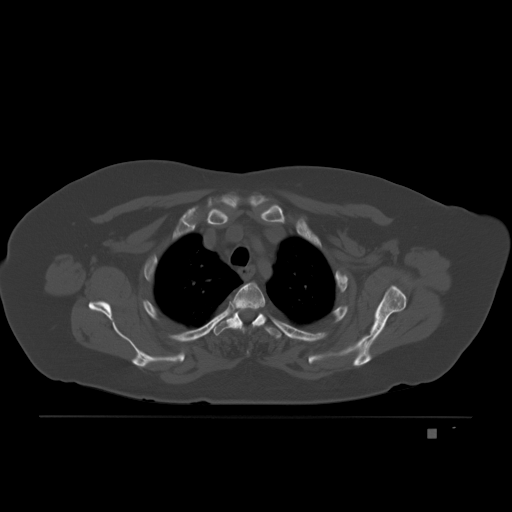
CT including the spine, one axial slice. Position 163 of 221 along the scan axis. Bone window (W 1800 / L 400 HU). 512 × 512 image matrix. Female patient, age 63 years. From the clinical record (not read from this slice): primary cancer: breast.
Annotated regions visible in this slice (semi-automatically segmented with operator editing):
- T3 vertebra: bounding box [x1, y1, x2, y2] px = [214, 292, 282, 339]